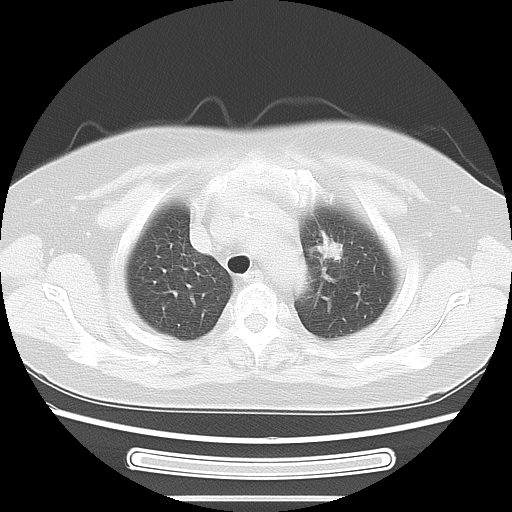
Chest CT, one axial slice; slice 47 of 58 in the series (ordered by position); reconstruction kernel LUNG; 120 kVp; lung window (W 1500 / L -600 HU); 512 × 512 image matrix, field of view 350 × 350 mm. Female patient, age 70 years. Case-level facts recorded for this patient, not image findings: clinical TNM (as recorded): T1c N0 M0; histopathological grade: G2-3.
Annotated regions visible in this slice (rectangle marked by the reading radiologist):
- lung tumour (recorded histology: adenocarcinoma): bounding box (x1, y1, x2, y2) in pixels: (315, 226, 359, 274)